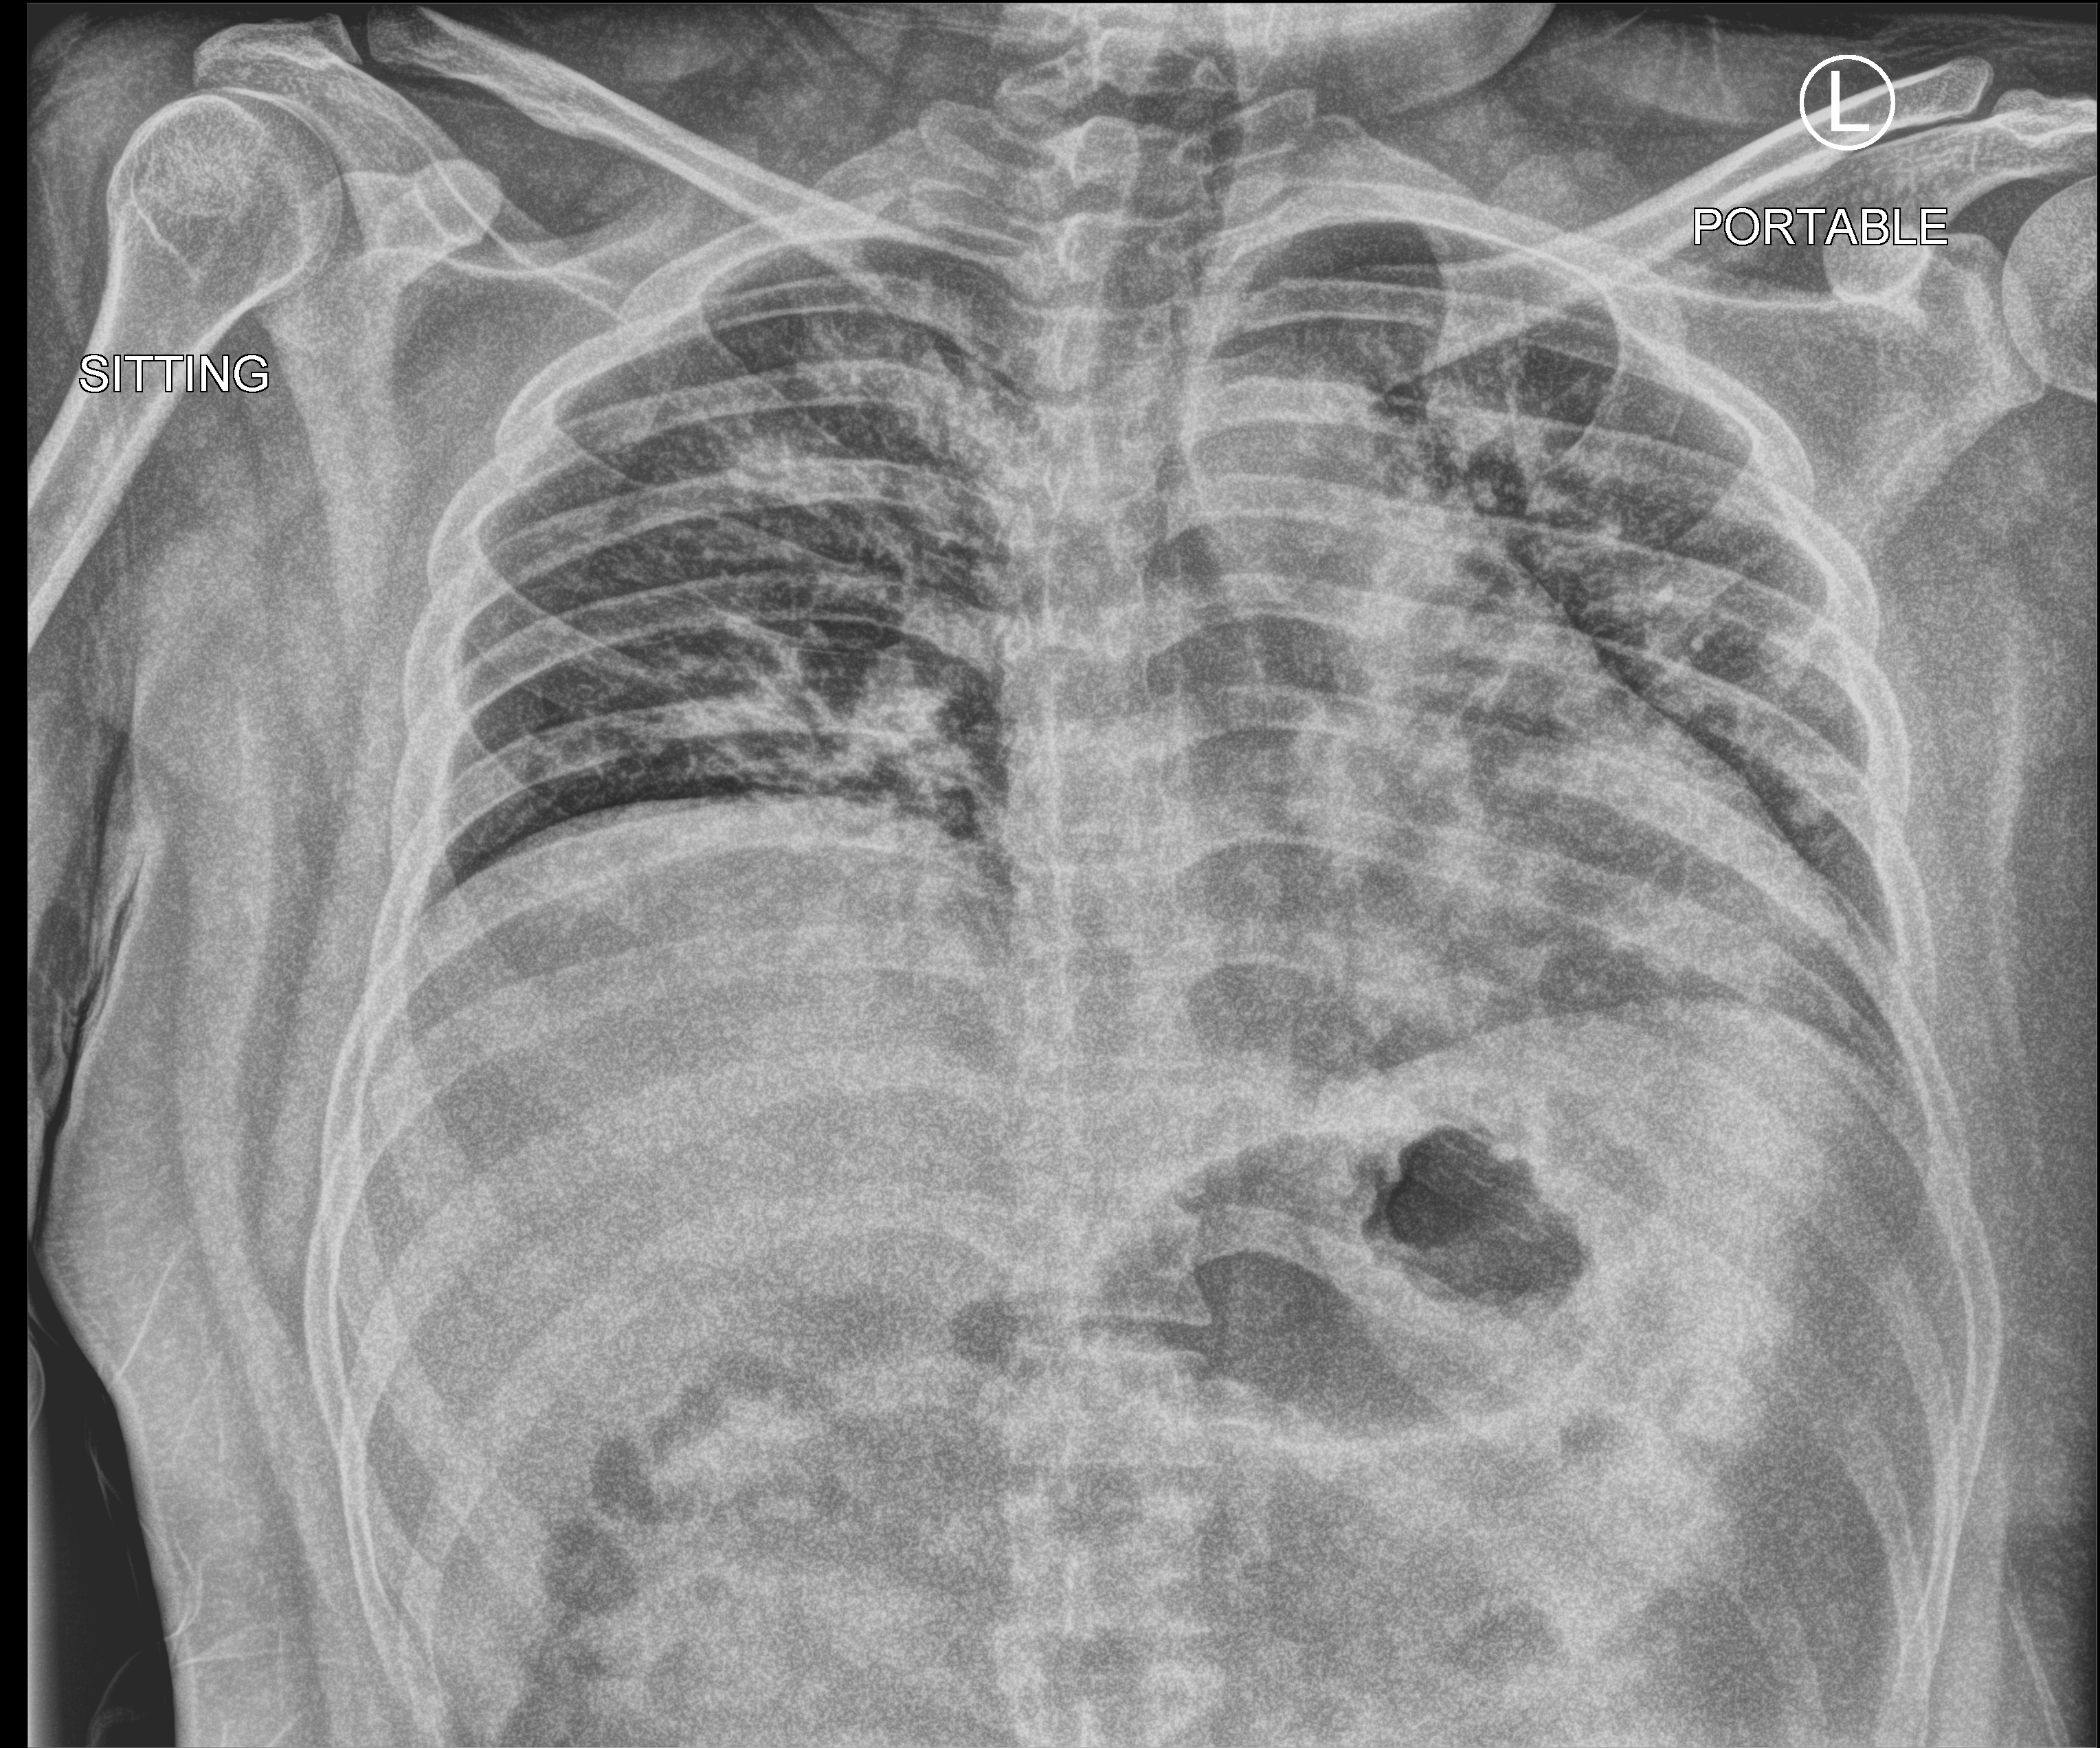
Portable chest radiograph, anteroposterior (AP) projection. Male patient hospitalised with COVID-19, age 18–59 years.
From the hospital-stay record, not from the radiograph (when in the stay this image was taken is not recorded): other chronic lung disease (admission record): no; mechanically ventilated during this hospital stay: no; smoking status (admission record): never.